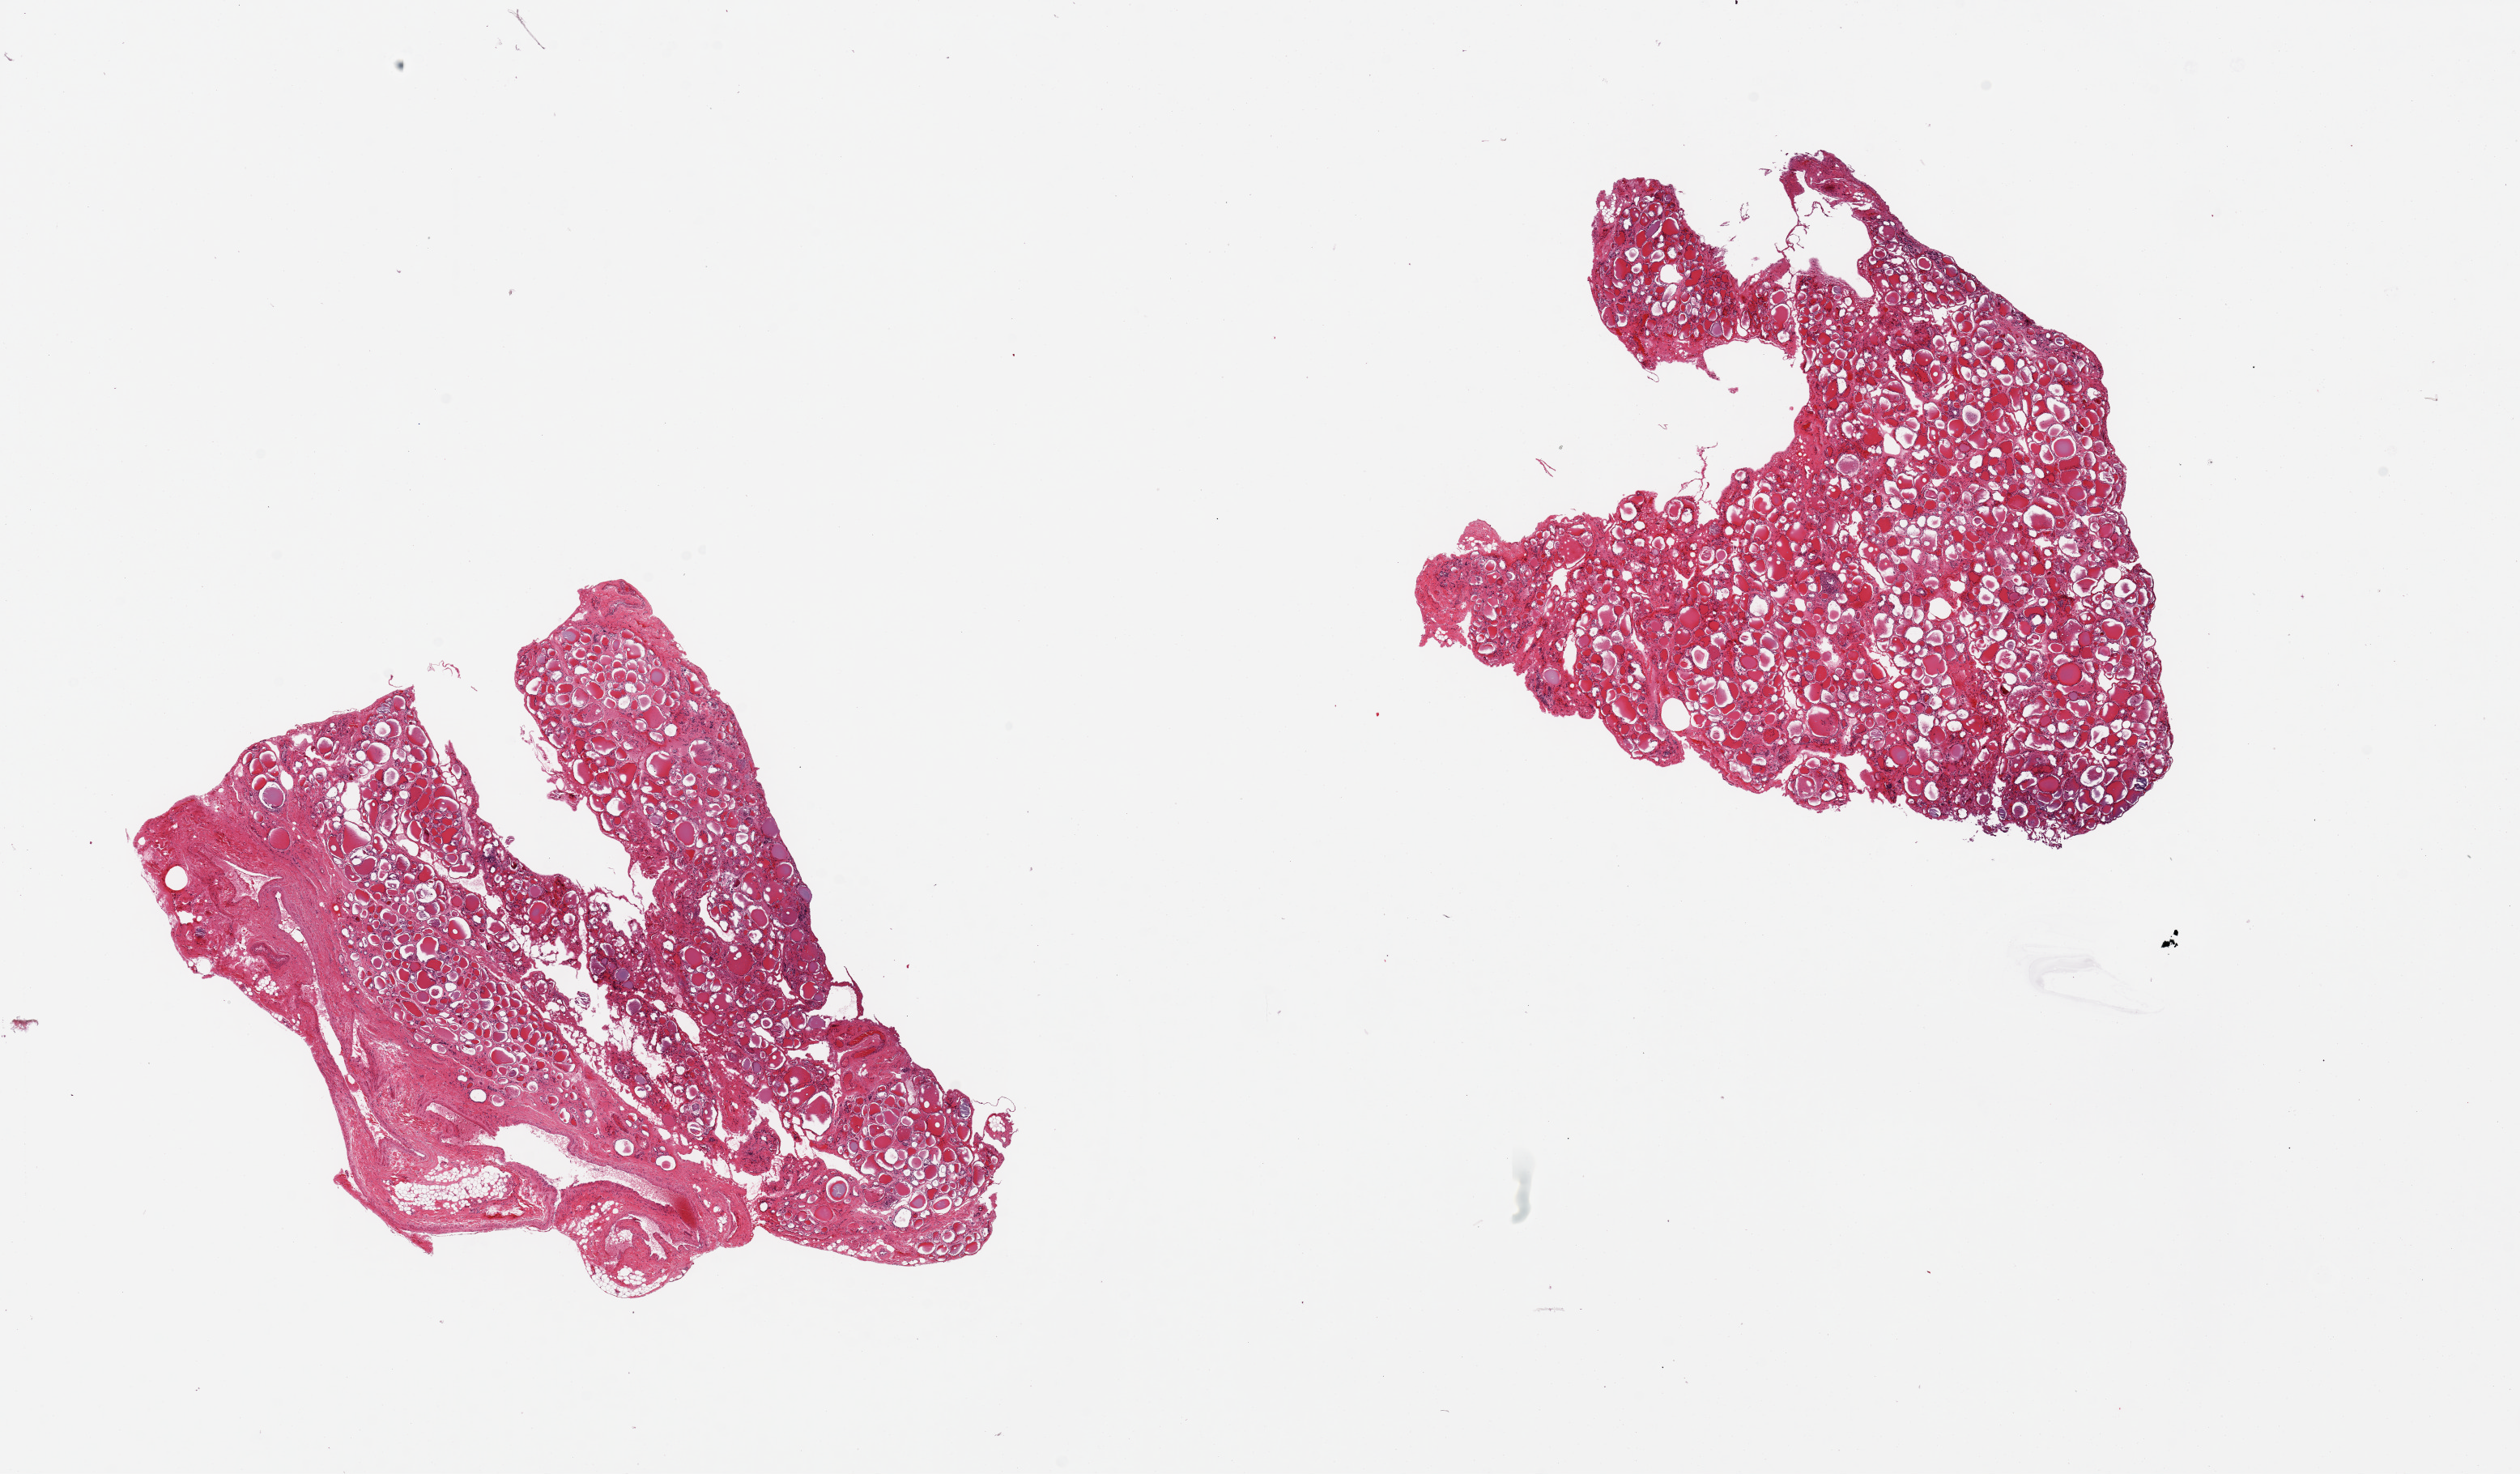
Haematoxylin and eosin whole-slide image, low-resolution overview of the scanned area, about 24.6 x 14.4 mm (slide scanned at 20x); PAXgene-fixed paraffin-embedded (PFPE) section; section of thyroid (target tissue); tissue donor sample. Donor sex: male.
• reviewer comment on this tissue sample: 2 pieces; 25% of 1 piece is fibroadipose and vascular tissue at one side